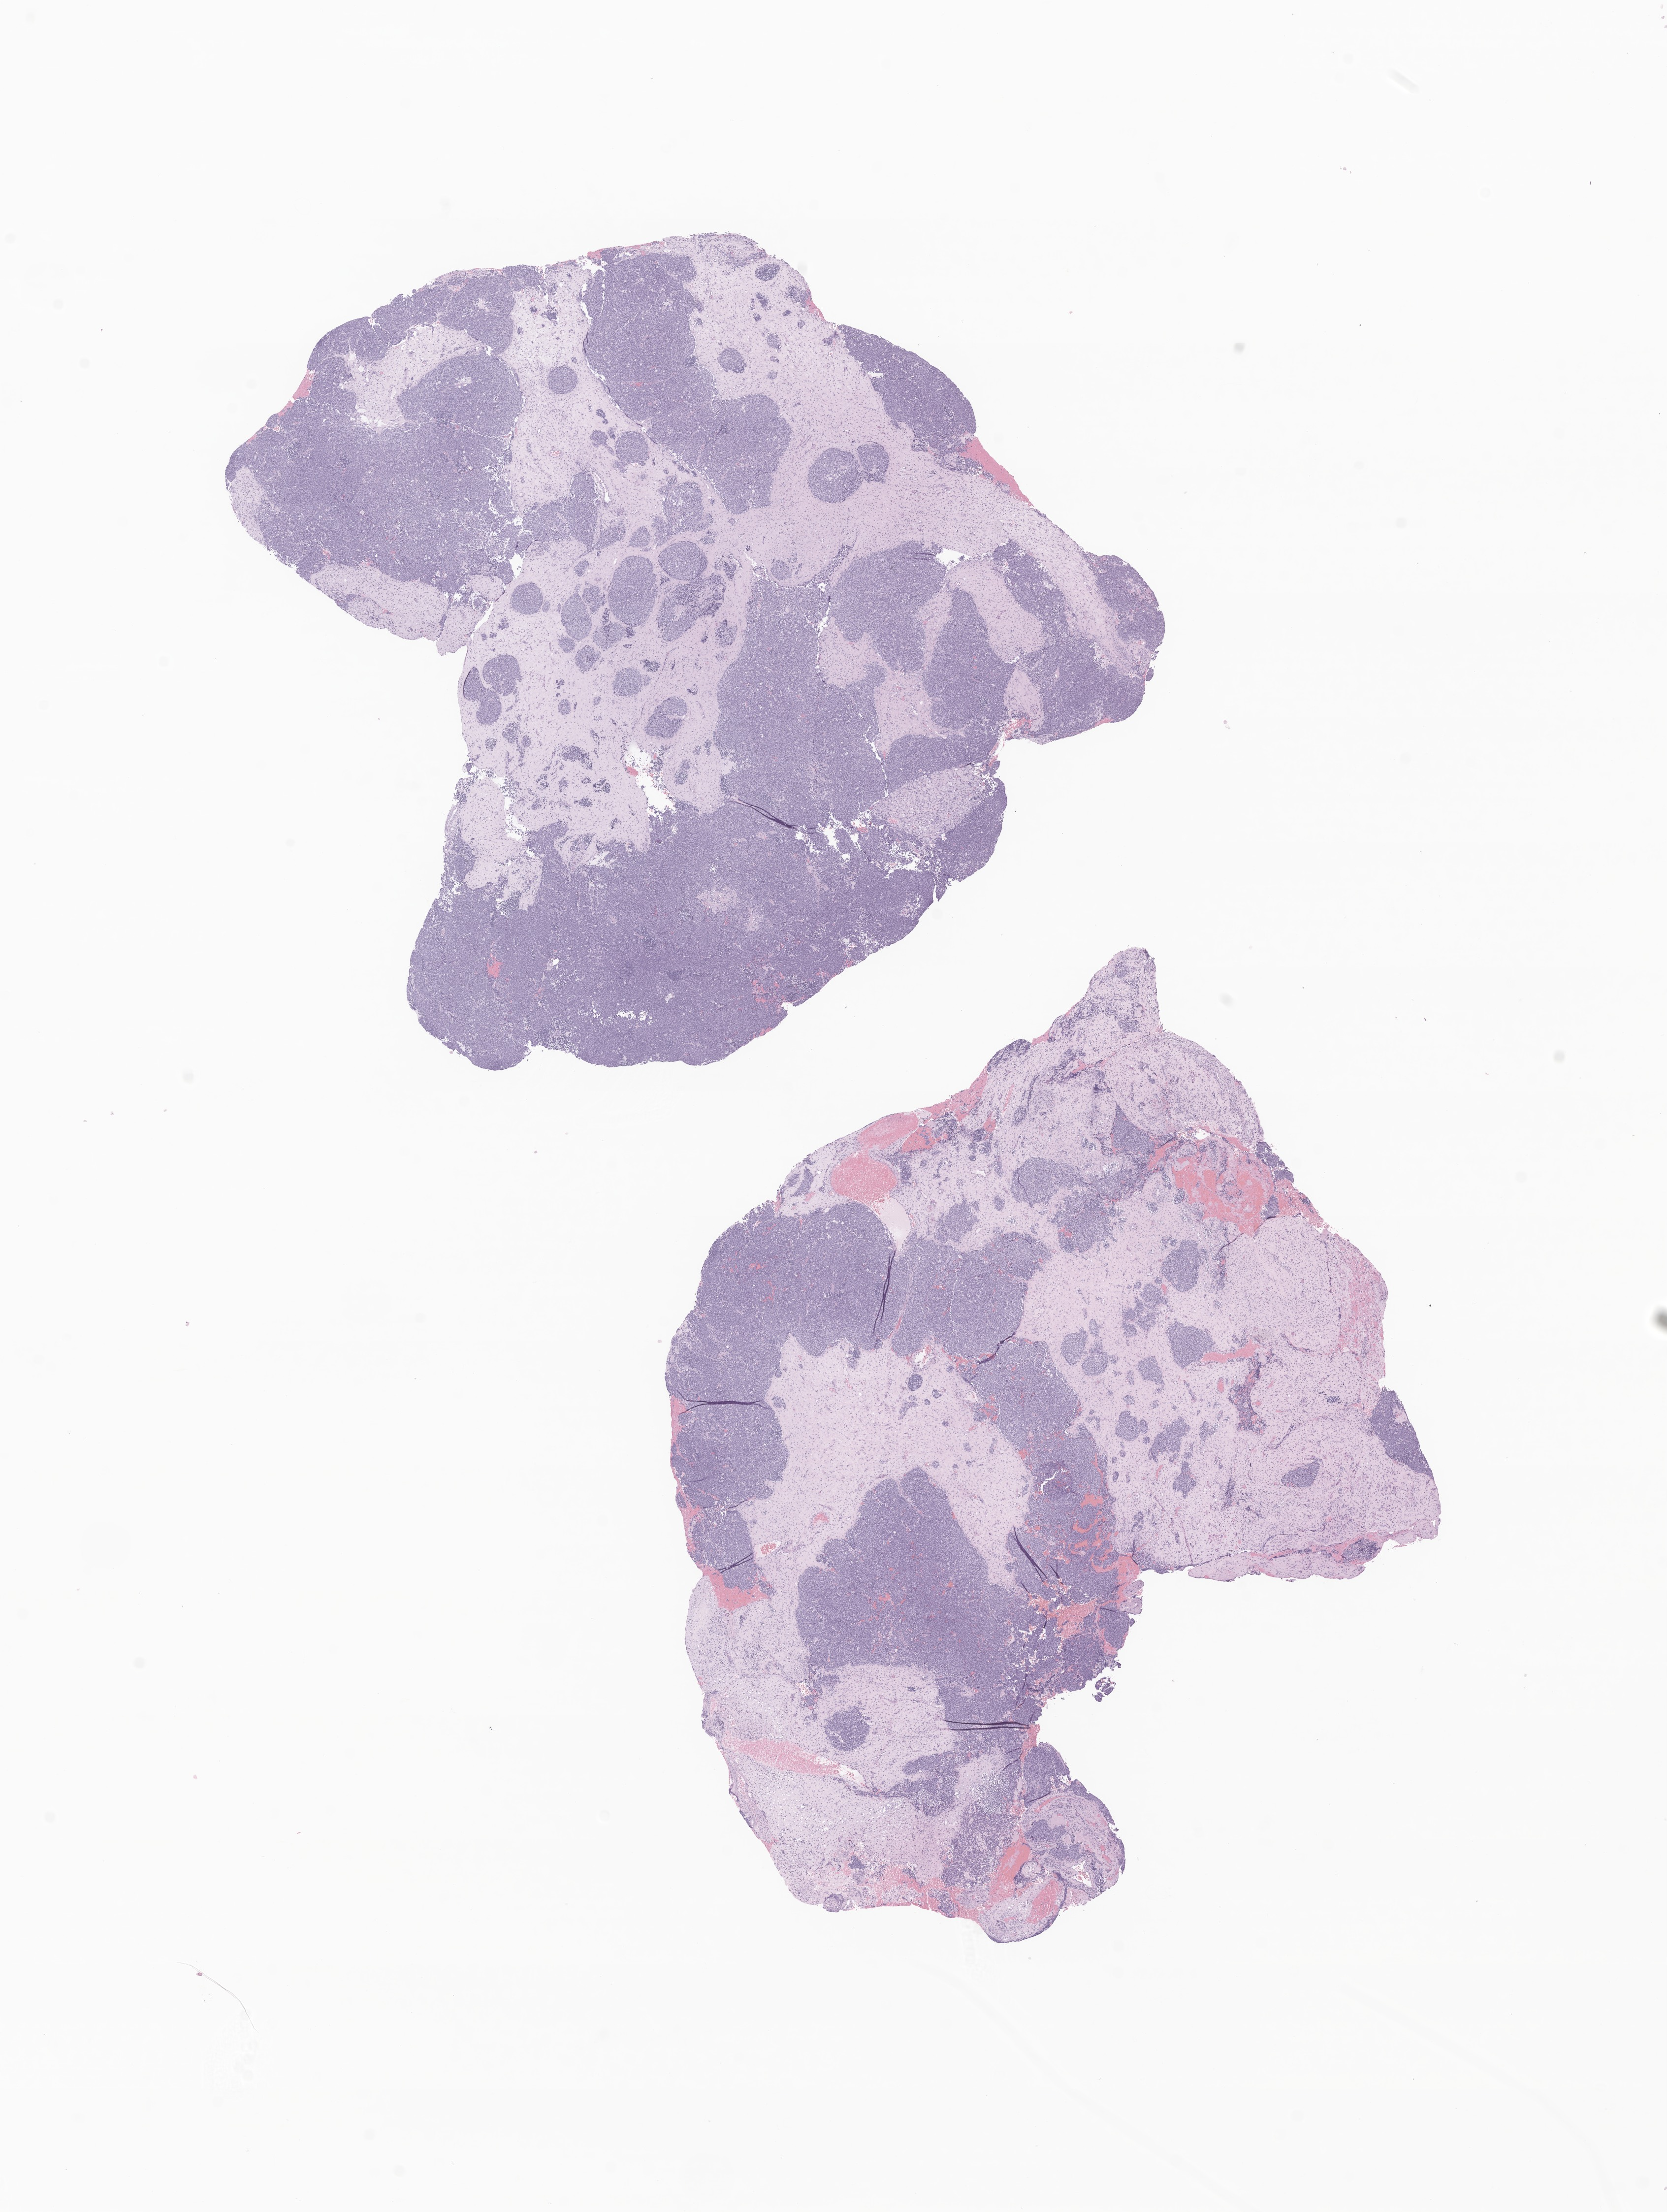
H&E whole-slide image of tumor tissue from the brain, whole scanned area (about 14.3 x 18.9 mm) shown as a low-resolution overview, formalin-fixed paraffin-embedded section. Female patient, age 179 months.
Recorded diagnosis: Medulloblastoma, NOS.